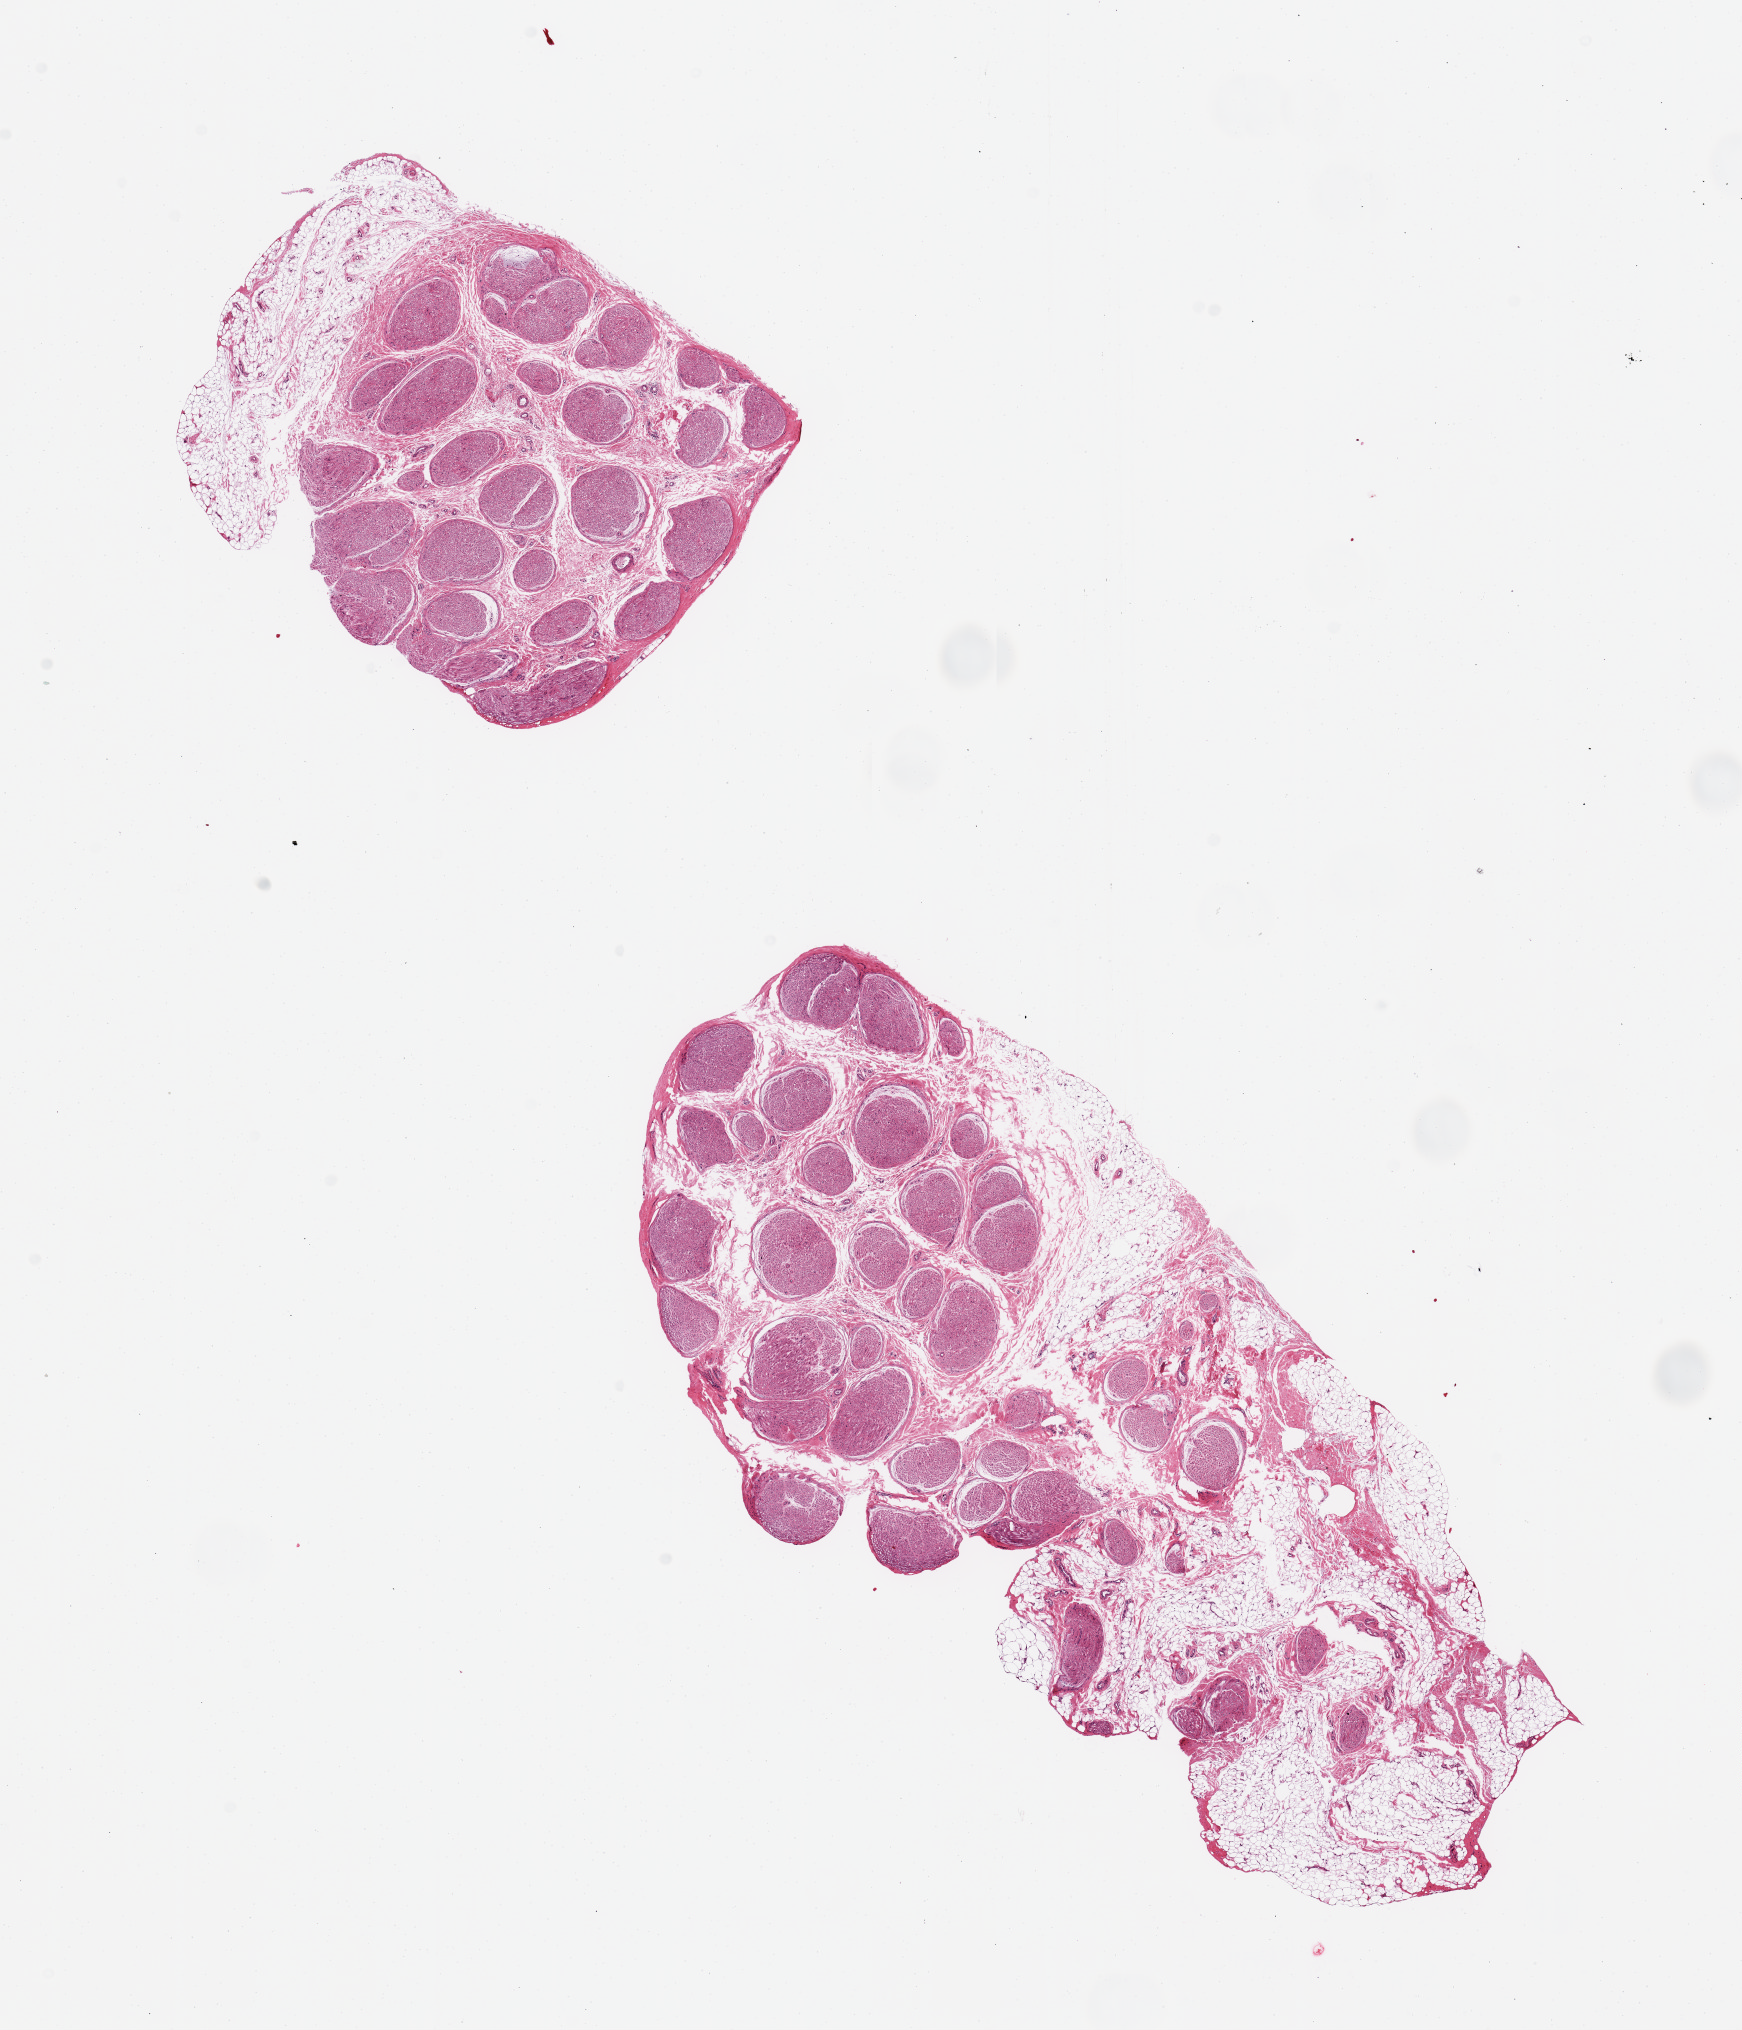
Hematoxylin and eosin (H&E) whole-slide image, brightfield — a low-resolution overview of the entire scanned area, about 13.8 x 16.1 mm; PAXgene-fixed paraffin-embedded (PFPE) section; section of tibial nerve (target tissue); tissue donor sample. Donor sex: female.
Review note (as recorded): 2 pieces, abundant adherent fat ~40% of tissue, sample with care.